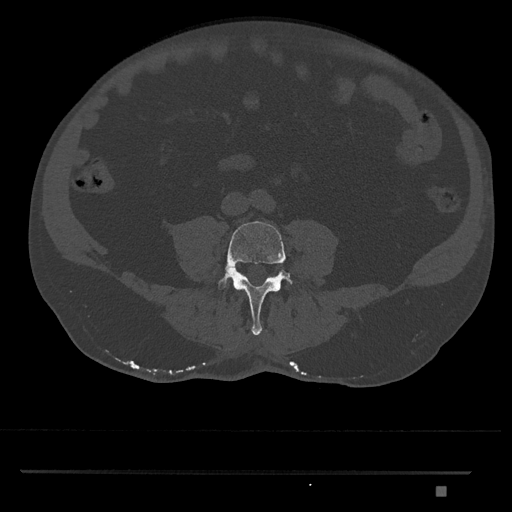
CT including the spine, one axial slice. Reconstruction kernel Br40s/3. 120 kVp. Bone window (W 1800 / L 400 HU). 0.5 mm slice thickness. 512 × 512 image matrix, field of view 429 × 429 mm. Patient: male, 65 years. From the clinical record (not read from this slice): primary cancer: prostate.
Outlined on this slice (semi-automatic segmentation, software-assisted and operator-edited):
- L4 vertebra: bounding box [x1, y1, x2, y2] px = [217, 221, 293, 336]